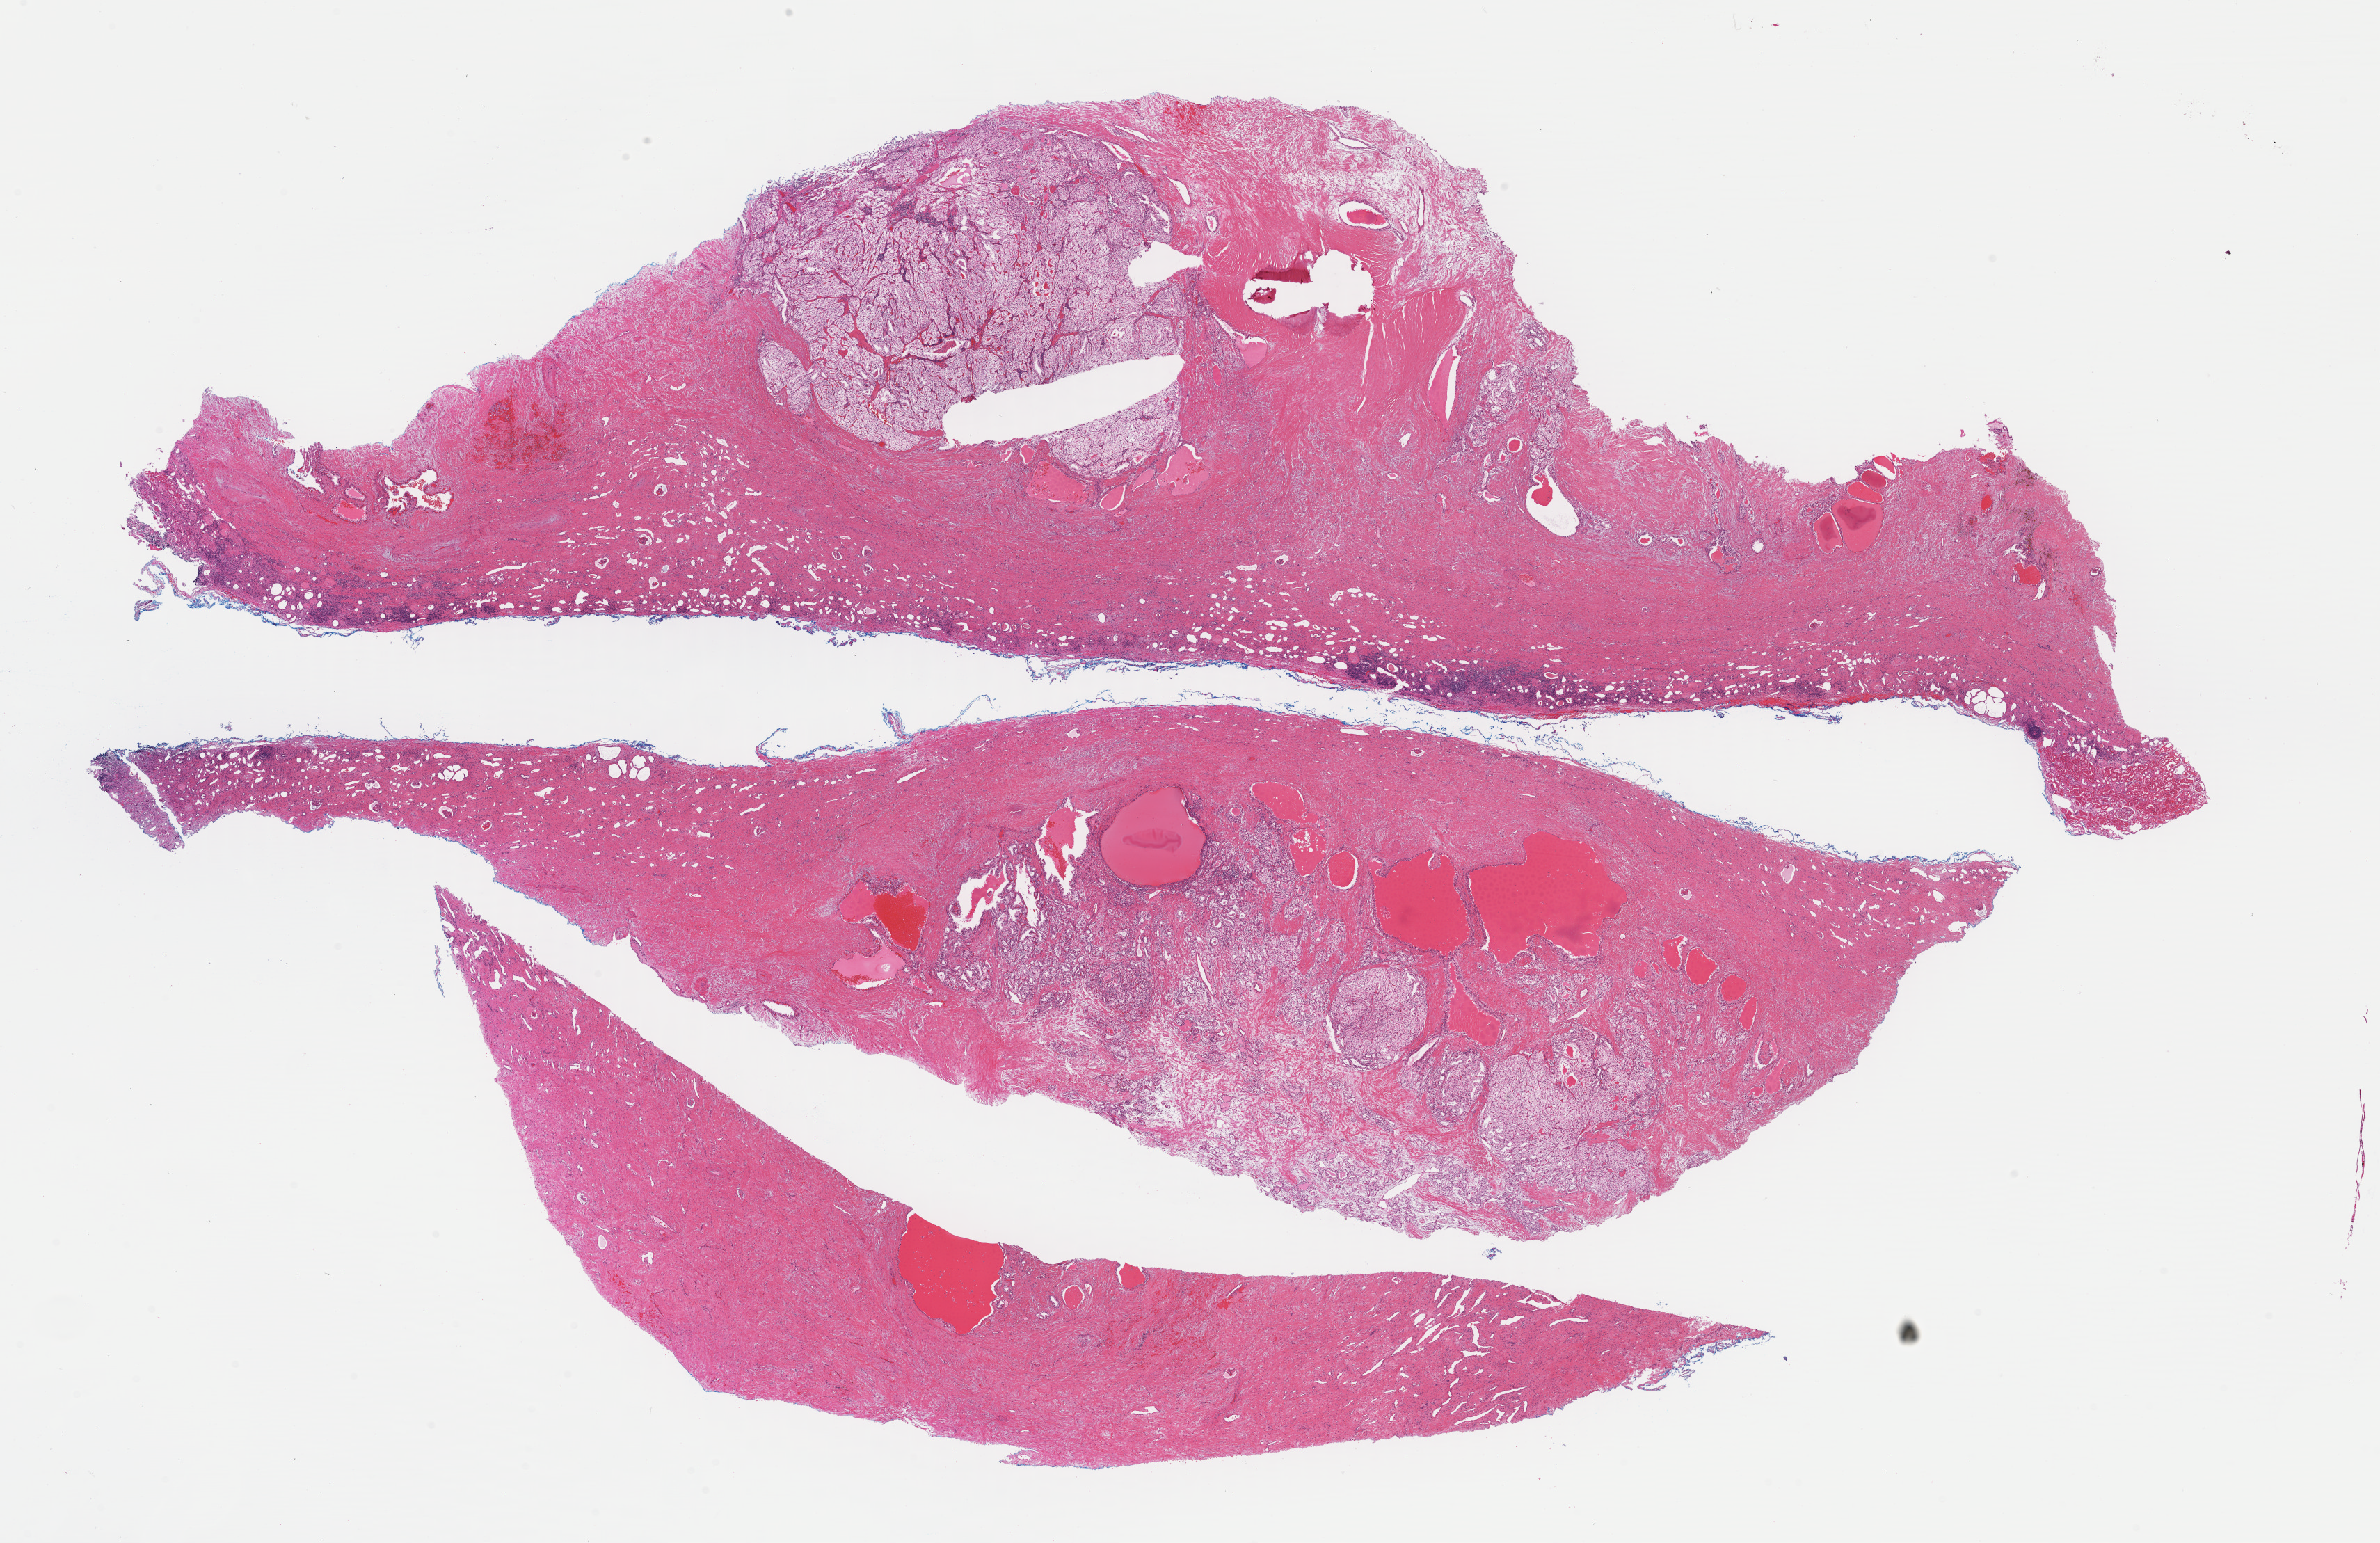
Digitized H&E-stained tissue section (whole slide), low-resolution overview of the scanned area, about 27.0 x 17.5 mm (slide scanned at 40x), FFPE section, kidney, primary tumour sample. Male patient; age at initial diagnosis 53 years. Histologic grade: G2 (moderately differentiated).
AJCC pathologic stage: I. Pathologic diagnosis: Clear cell adenocarcinoma, NOS. TNM: T1a NX MX.